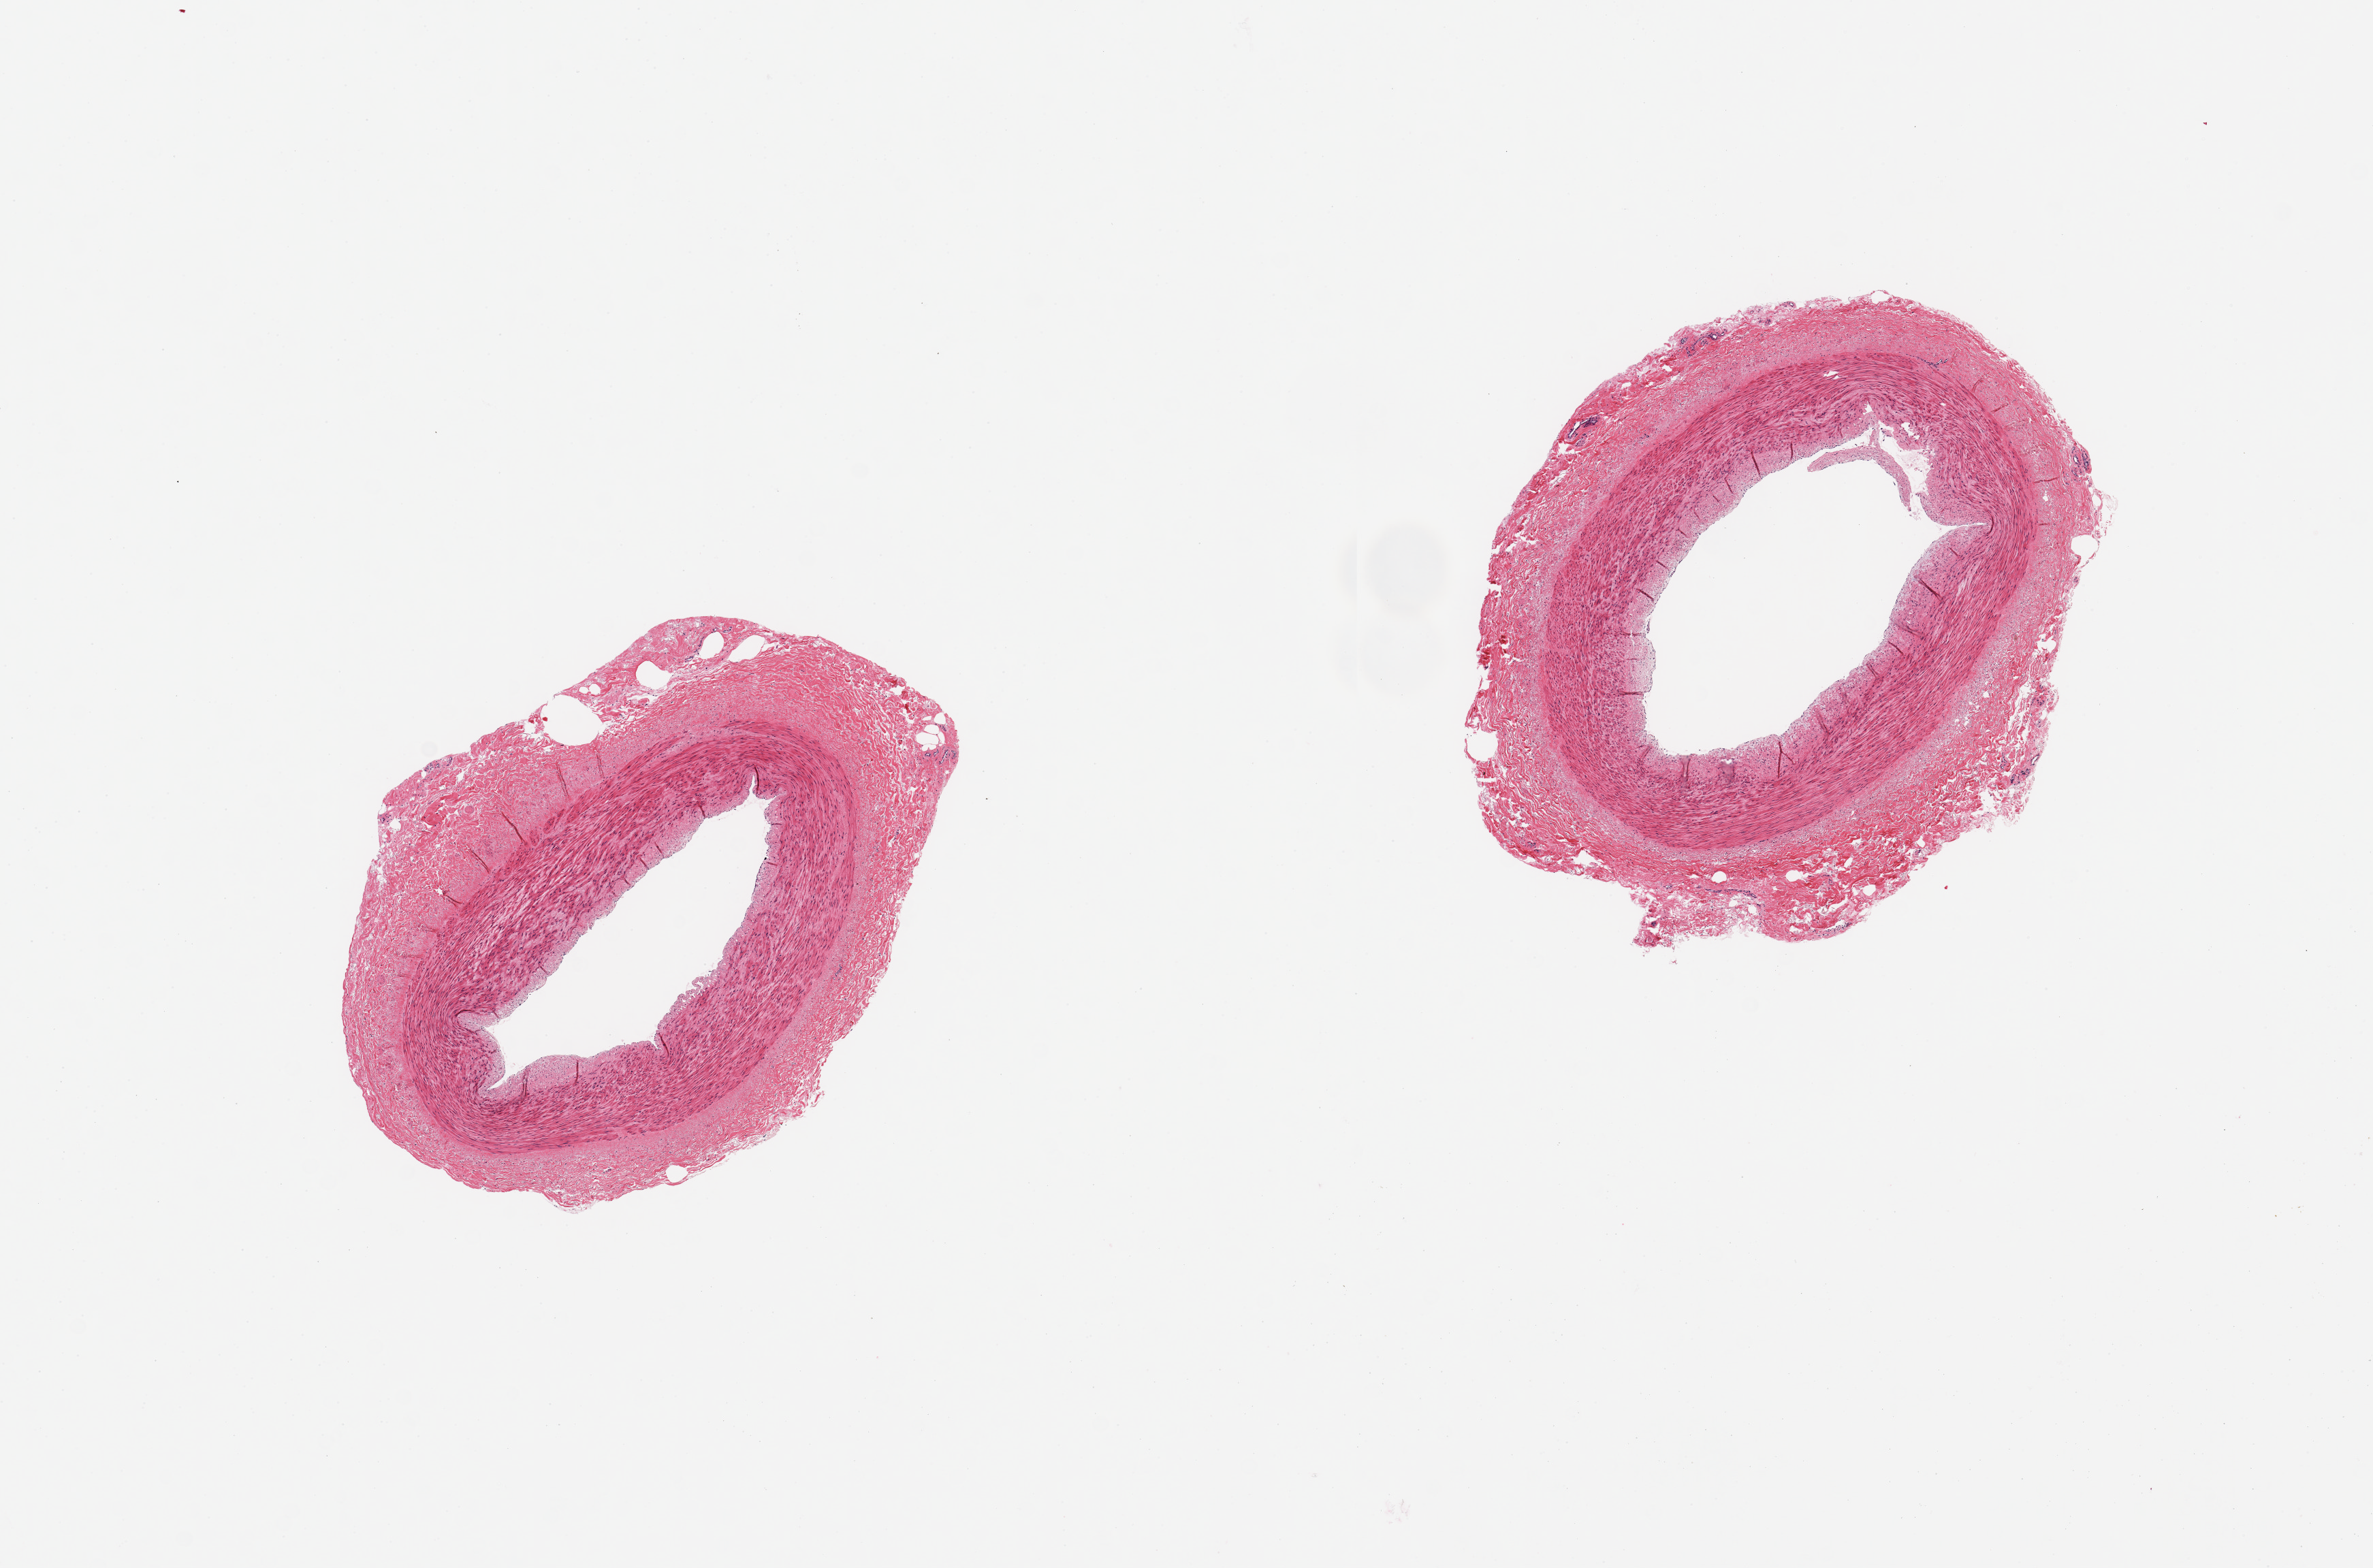
Whole-slide image, hematoxylin and eosin (H&E) stain, brightfield, whole scanned area (about 13.8 x 9.1 mm, from a 20x scan) shown as a low-resolution overview, PAXgene-fixed paraffin-embedded (PFPE) section, section of tibial artery (target tissue), donor tissue sample. Male donor.
Pathologist's review note for this sample: 2 pieces; some intimal thickening/sclerosis.